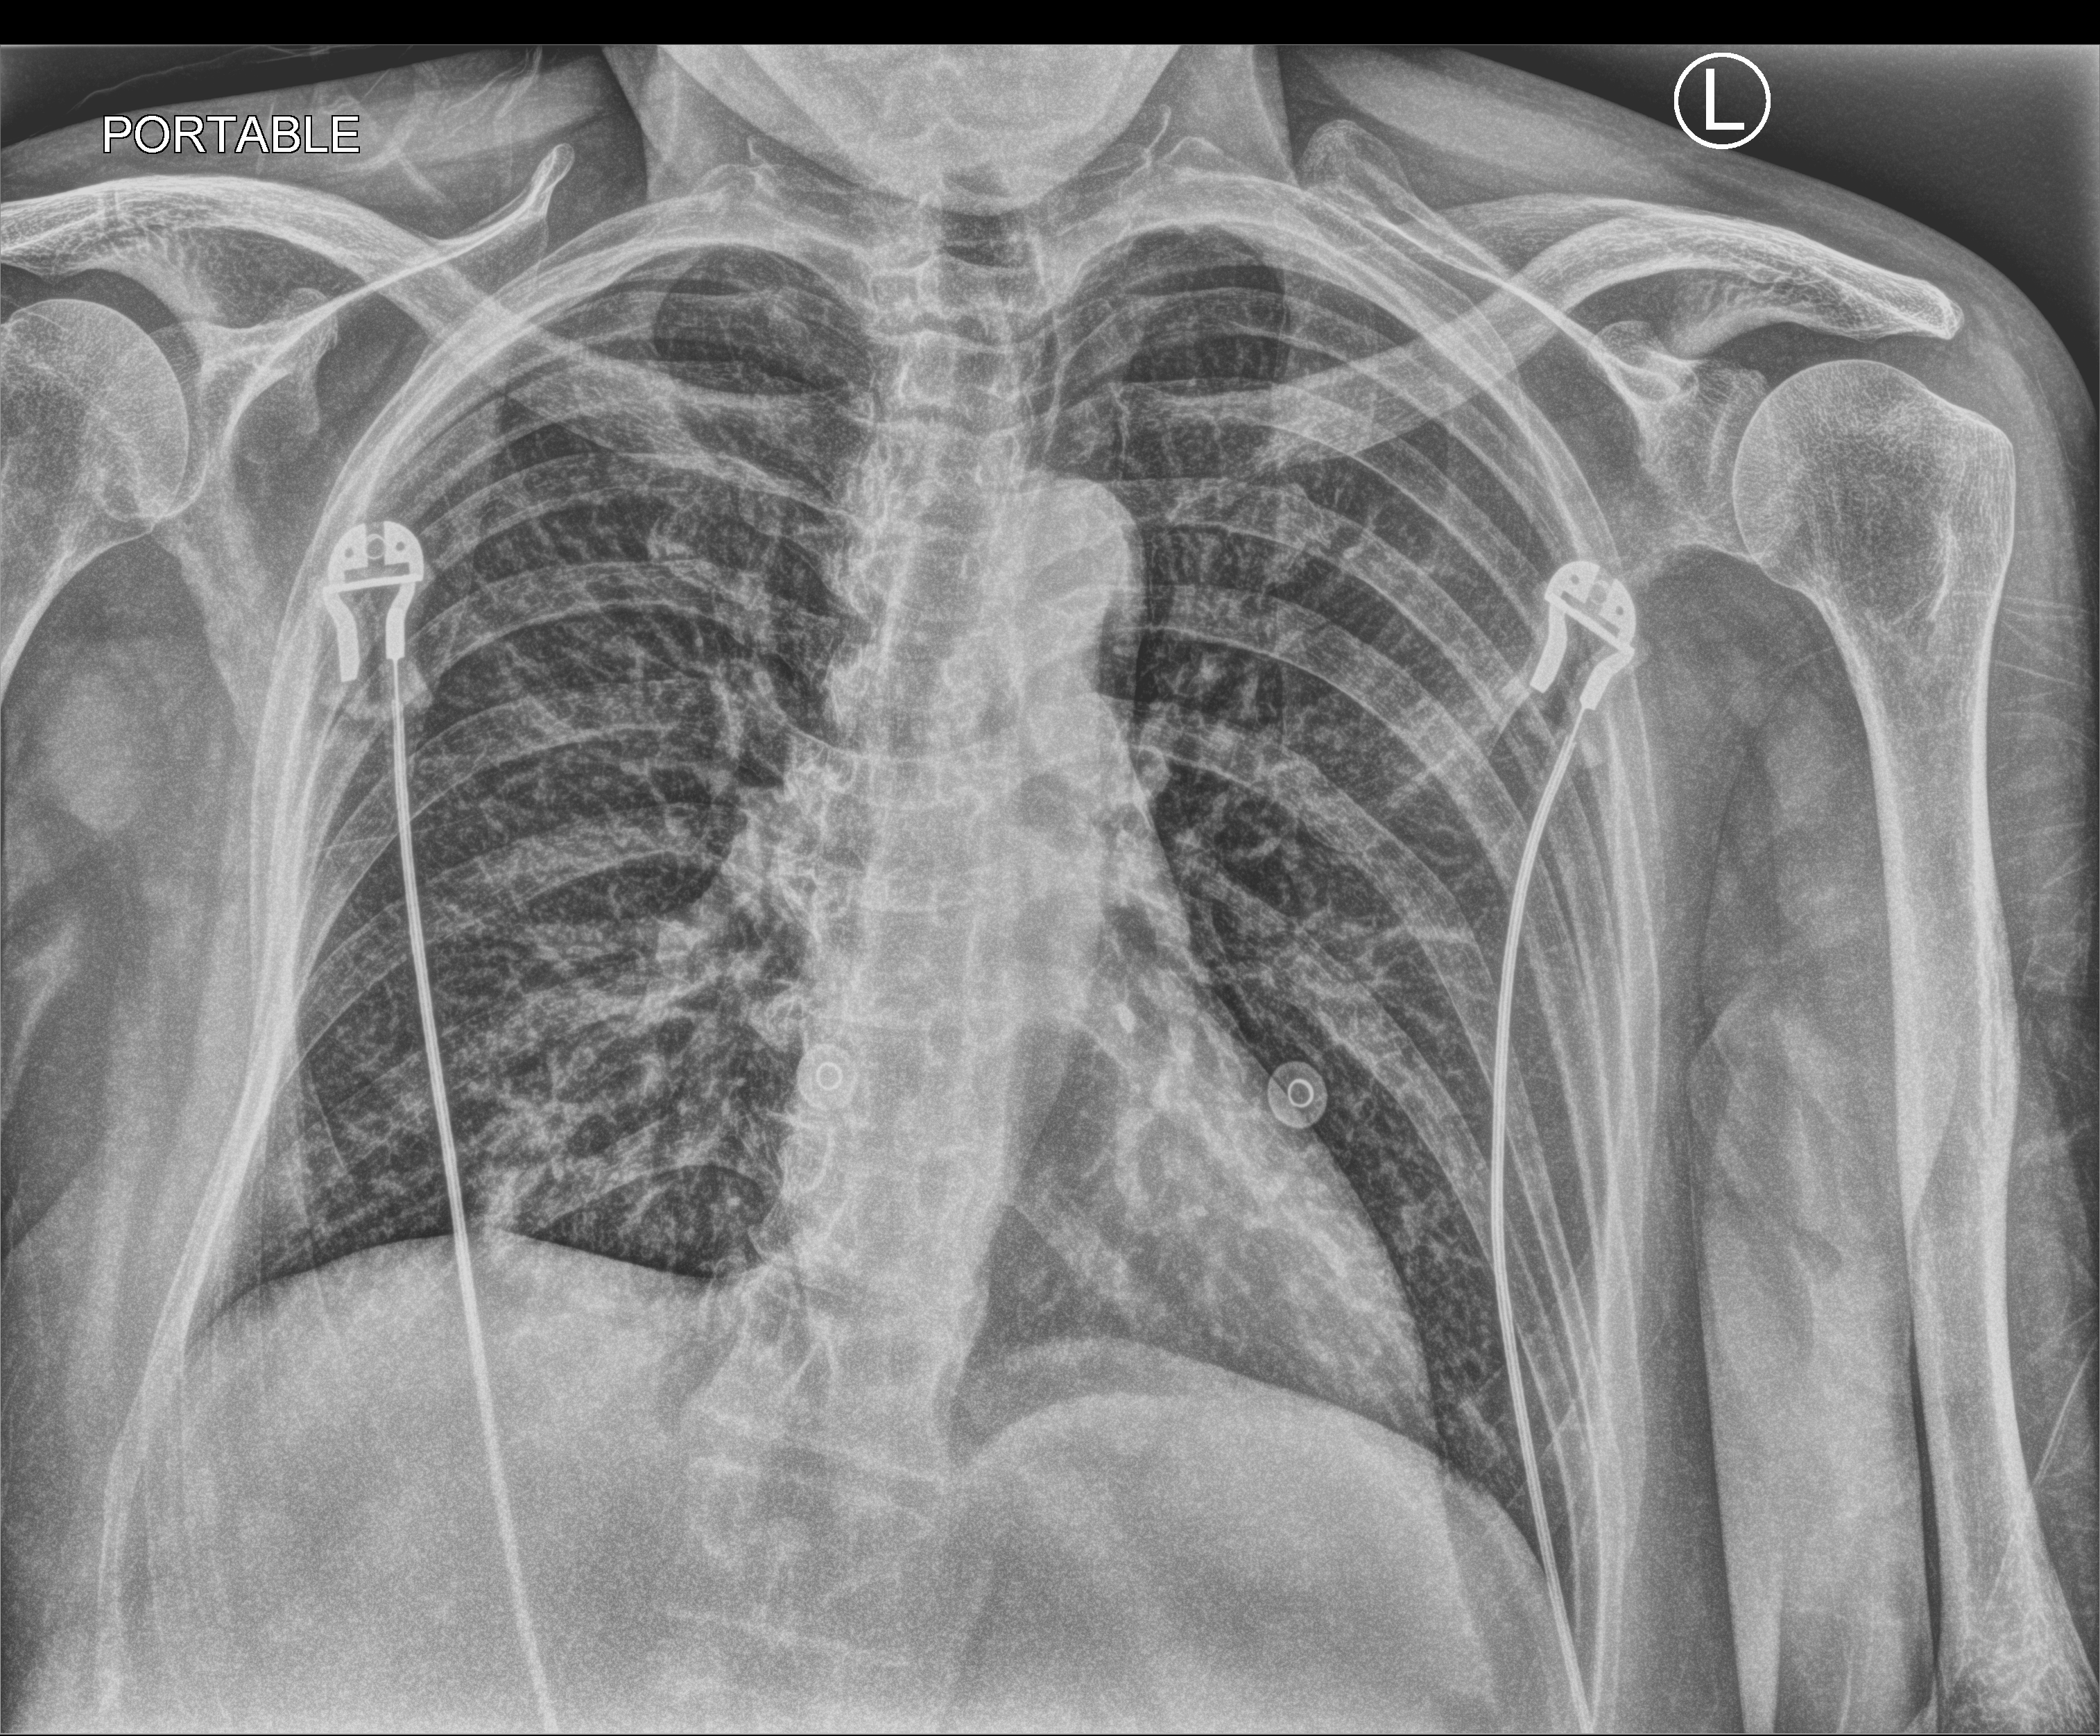
Portable chest radiograph. Patient hospitalised with COVID-19; female, aged 60–74 years.
Hospital-stay facts (about this admission, not read from this image; timing relative to this image not recorded): admitted to intensive care during this hospital stay: no; hypertension (admission record): yes.